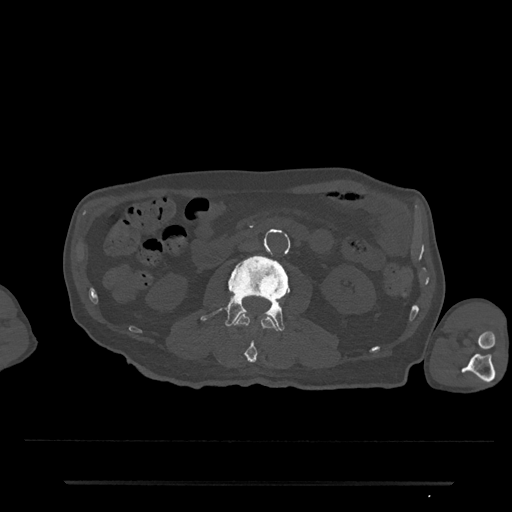
CT including the spine, one axial slice; position 15 of 797 along the scan axis; bone window (W 1800 / L 400 HU); 512 × 512 image matrix, field of view 427 × 427 mm. Patient: male, 74 years. Case-level facts recorded for this patient, not image findings: primary cancer: prostate.
Structures marked on this image (semi-automatic segmentation, software-assisted and operator-edited):
- L2 vertebra: bounding box [x1, y1, x2, y2] px = [234, 314, 279, 363]
- L3 vertebra: [200, 256, 290, 331]